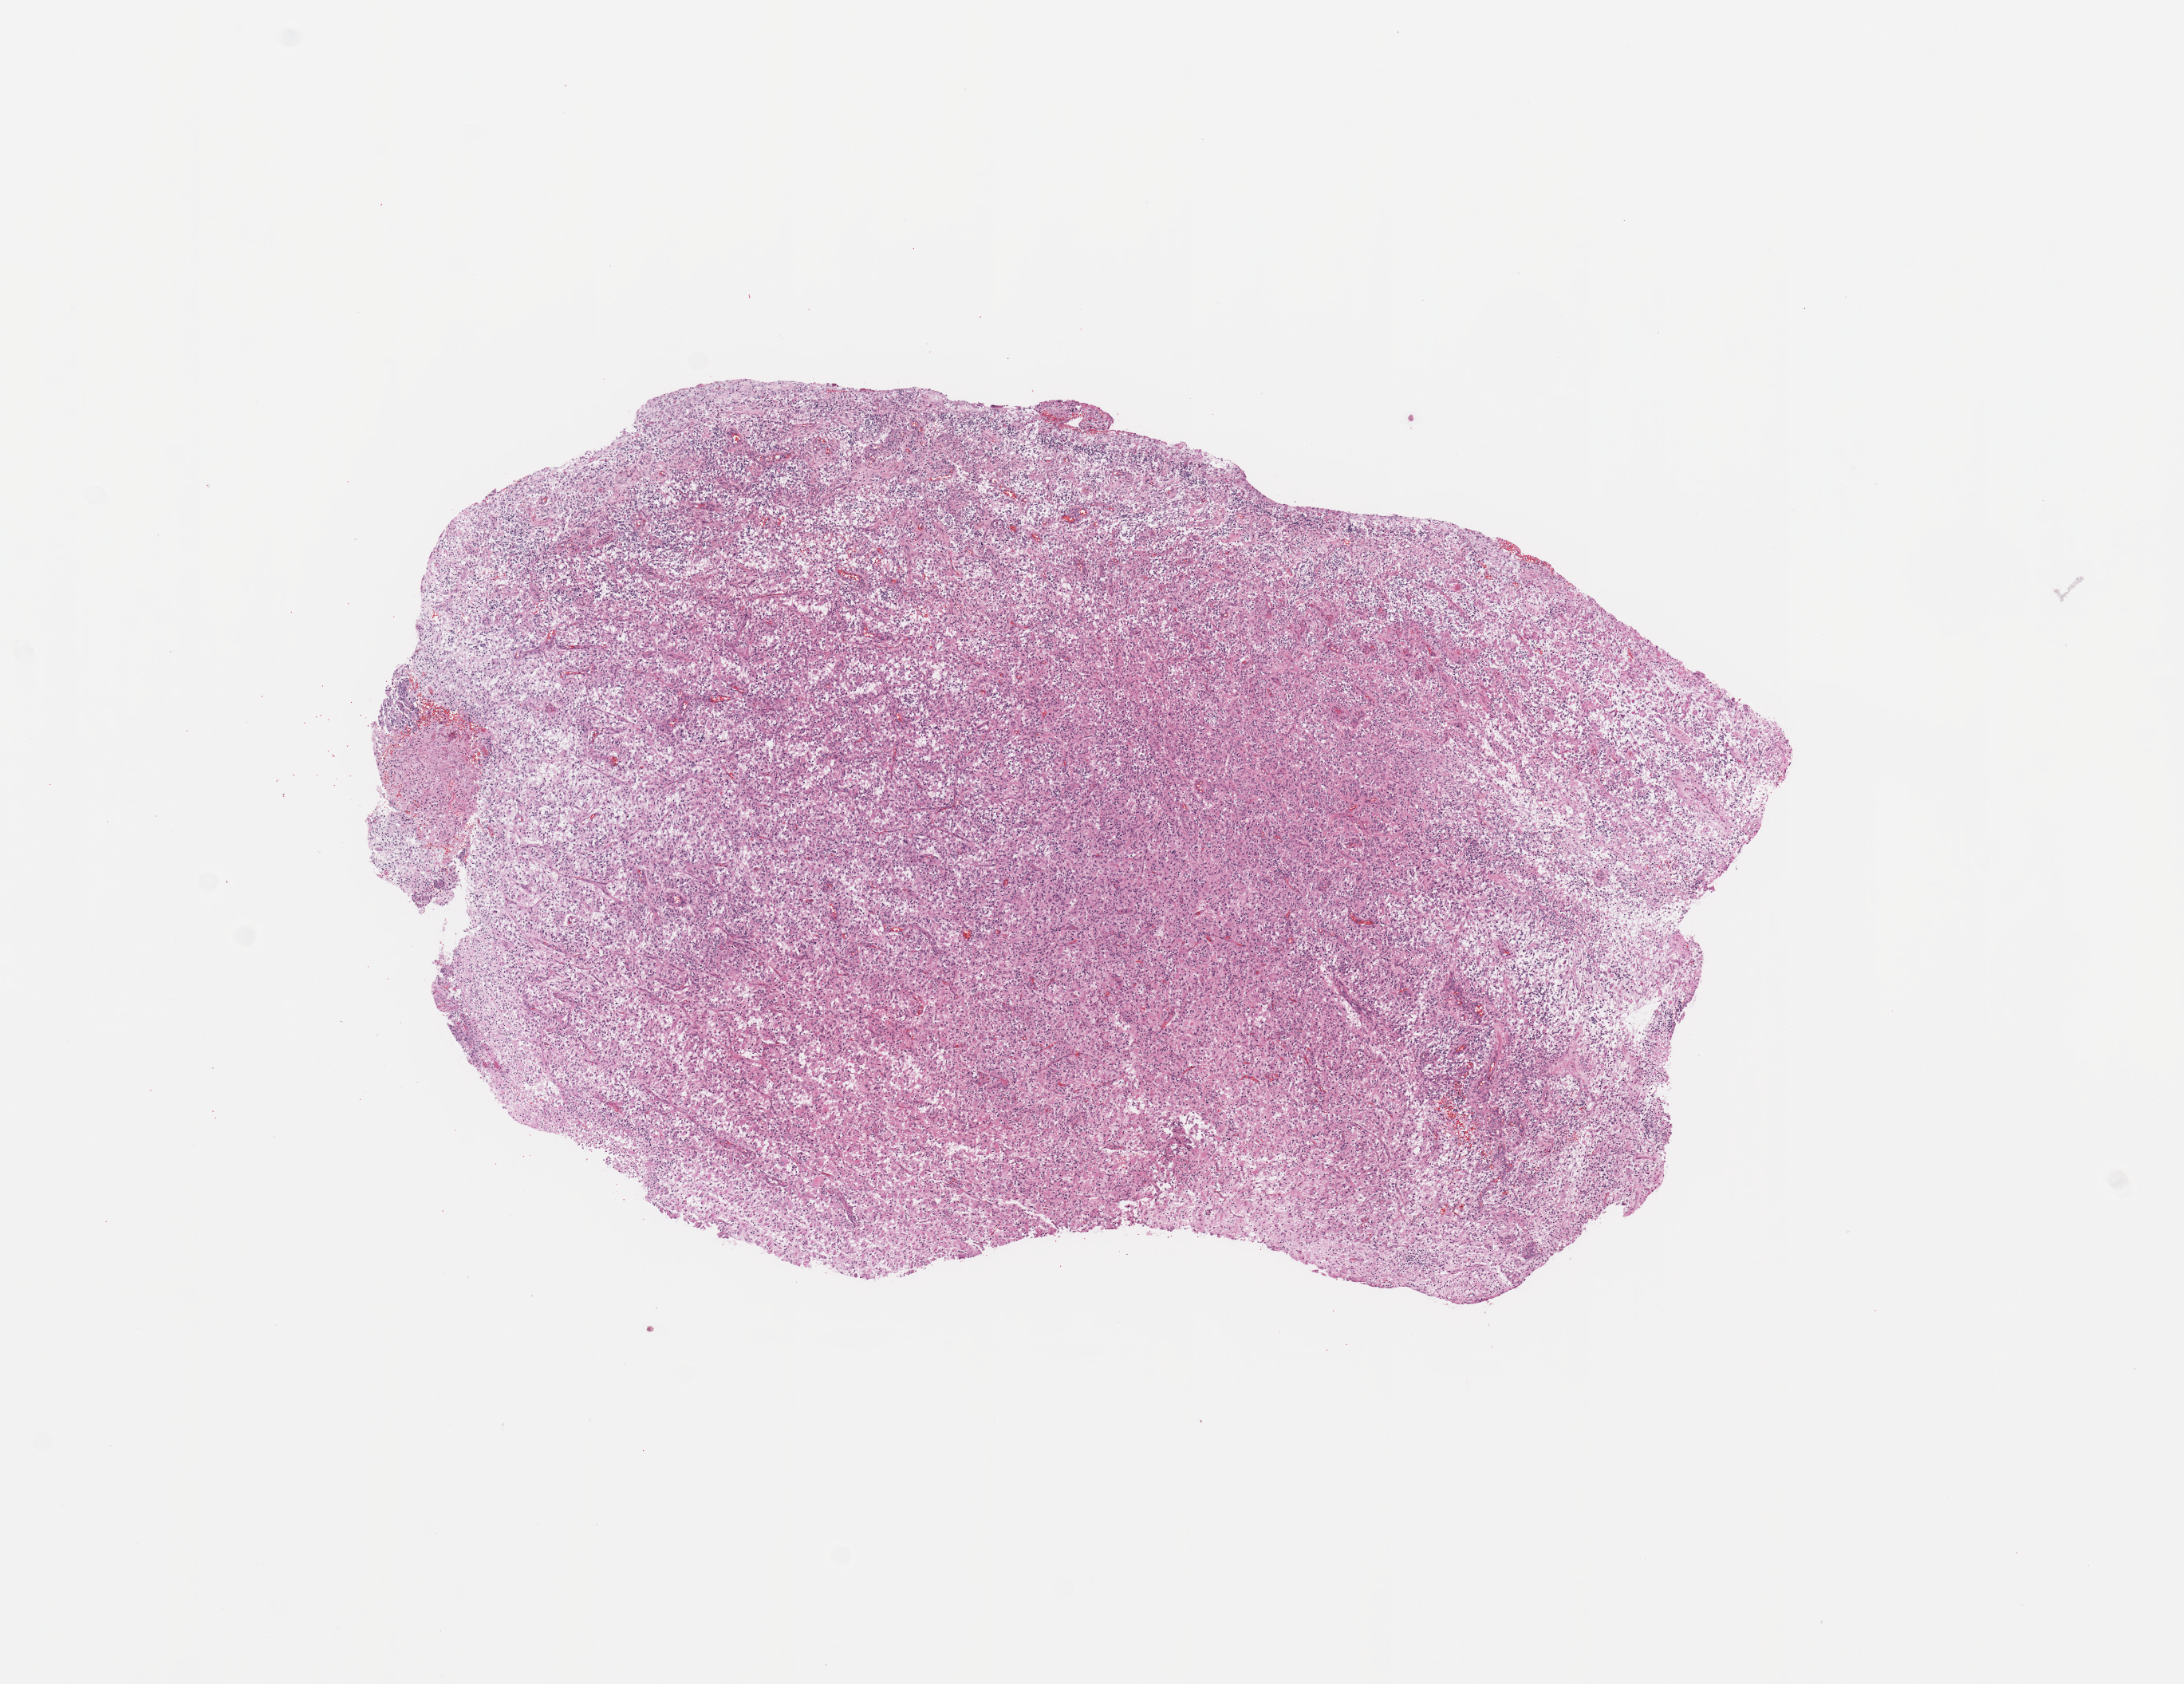
H&E whole-slide image — a low-resolution overview of the entire scanned area, about 10.8 x 8.3 mm (from a 20x scan). Tumour tissue sample, sampled site: temporal cortex. Male, 50 y/o. Slide review estimates, as recorded: tumour nuclei 90%, necrosis 2%.
Histologic diagnosis: Glioblastoma.